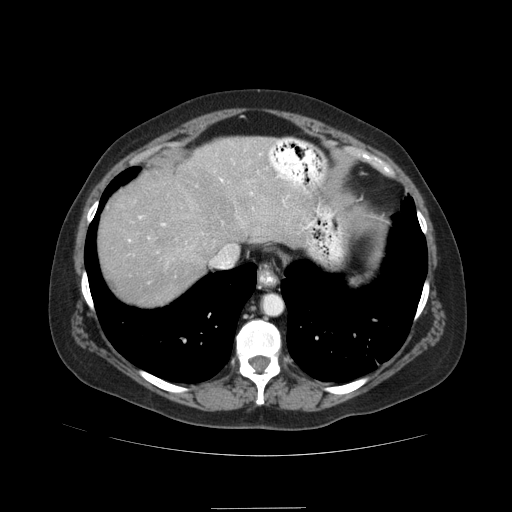
Contrast-enhanced abdominal CT (liver protocol), one axial slice. Position 74 of 89 along the scan axis. Soft-tissue window (W 400 / L 40 HU). 512 × 512 image matrix, field of view 400 × 400 mm. Case-level facts recorded for this patient, not image findings: diagnosis: hepatocellular carcinoma (patient treated with transarterial chemoembolisation; whether this scan precedes or follows treatment is not stated here); TNM stage (as recorded): Stage-IIIB; Child-Pugh class: A.
Structures marked on this image (semi-automatic segmentation, software-assisted and operator-edited):
- liver parenchyma outside the tumour (the mass and vessels are separate outlines, so this box may not span the whole liver): bounding box [x1, y1, x2, y2] px = [98, 136, 314, 306]
- liver vessels: [129, 179, 309, 241]